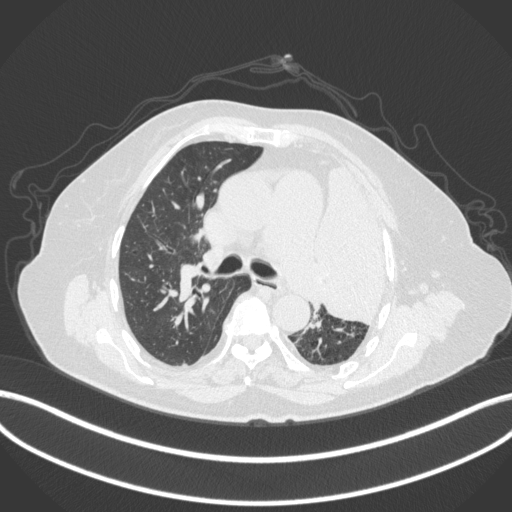
Chest CT, one axial slice. Position 247 of 399 along the scan axis. 120 kVp. Lung window (W 1500 / L -600 HU). 1 mm slice thickness. 512 × 512 image matrix, field of view 400 × 400 mm. Female patient, age 75 years. Case-level facts recorded for this patient, not image findings: clinical TNM (as recorded): T3 N3 M1.
Outlined on this slice (bounding box drawn by a radiologist):
- lung tumour (recorded histology: adenocarcinoma): bounding box <309,148,405,328> (left, top, right, bottom; pixels)